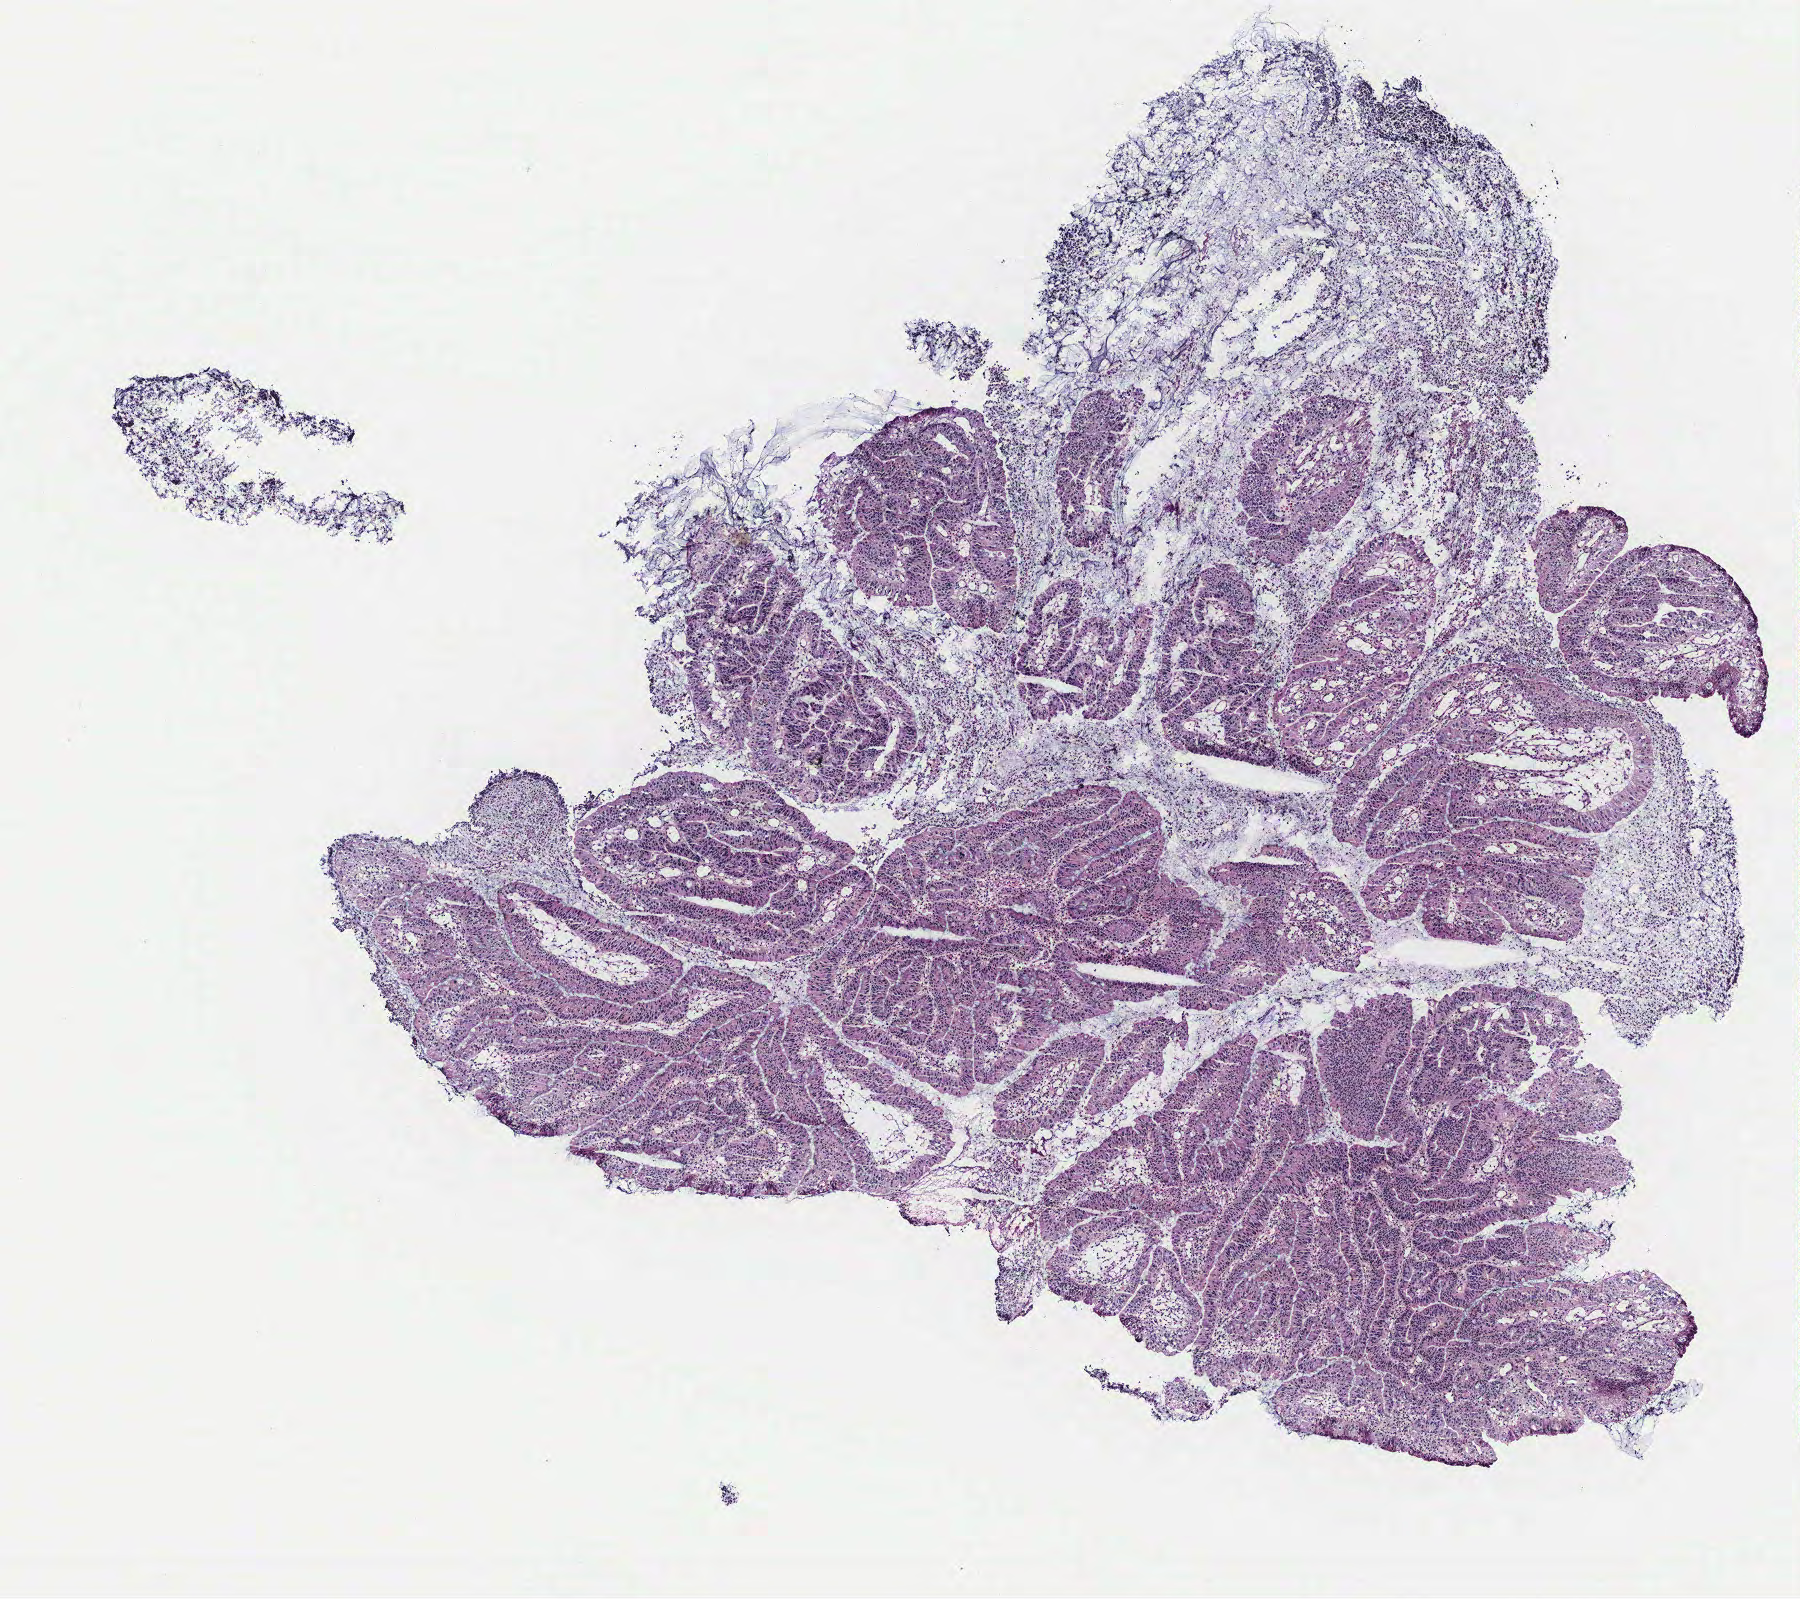
Whole-slide histology image, H&E-stained — a low-resolution overview of the entire scanned area, about 7.2 x 6.4 mm (acquisition: 40x scan); colon, tissue type not recorded.
Patient diagnosis (cohort enrolment): colon cancer (colon).